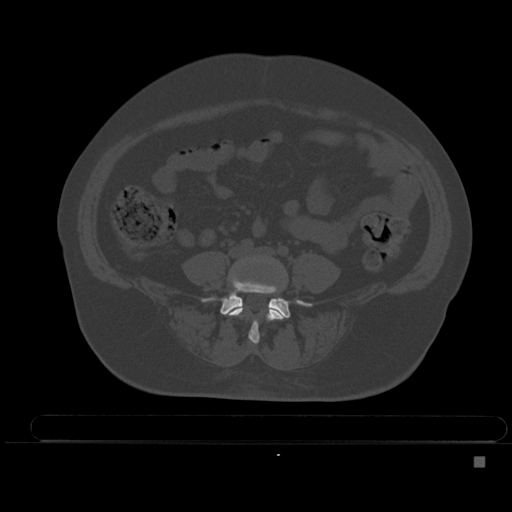
CT including the spine, one axial slice. Slice 118 of 495 in the series (ordered by position). Bone window (W 1800 / L 400 HU). 1.5 mm slice thickness. 512 × 512 image matrix, field of view 404 × 404 mm. Patient: female, 33 years. Case-level facts recorded for this patient, not image findings: primary cancer: breast.
Outlined on this slice (semi-automatic segmentation, software-assisted and operator-edited):
- L4 vertebra: bounding box <228,270,284,344> (left, top, right, bottom; pixels)
- L5 vertebra: <220,281,303,318>